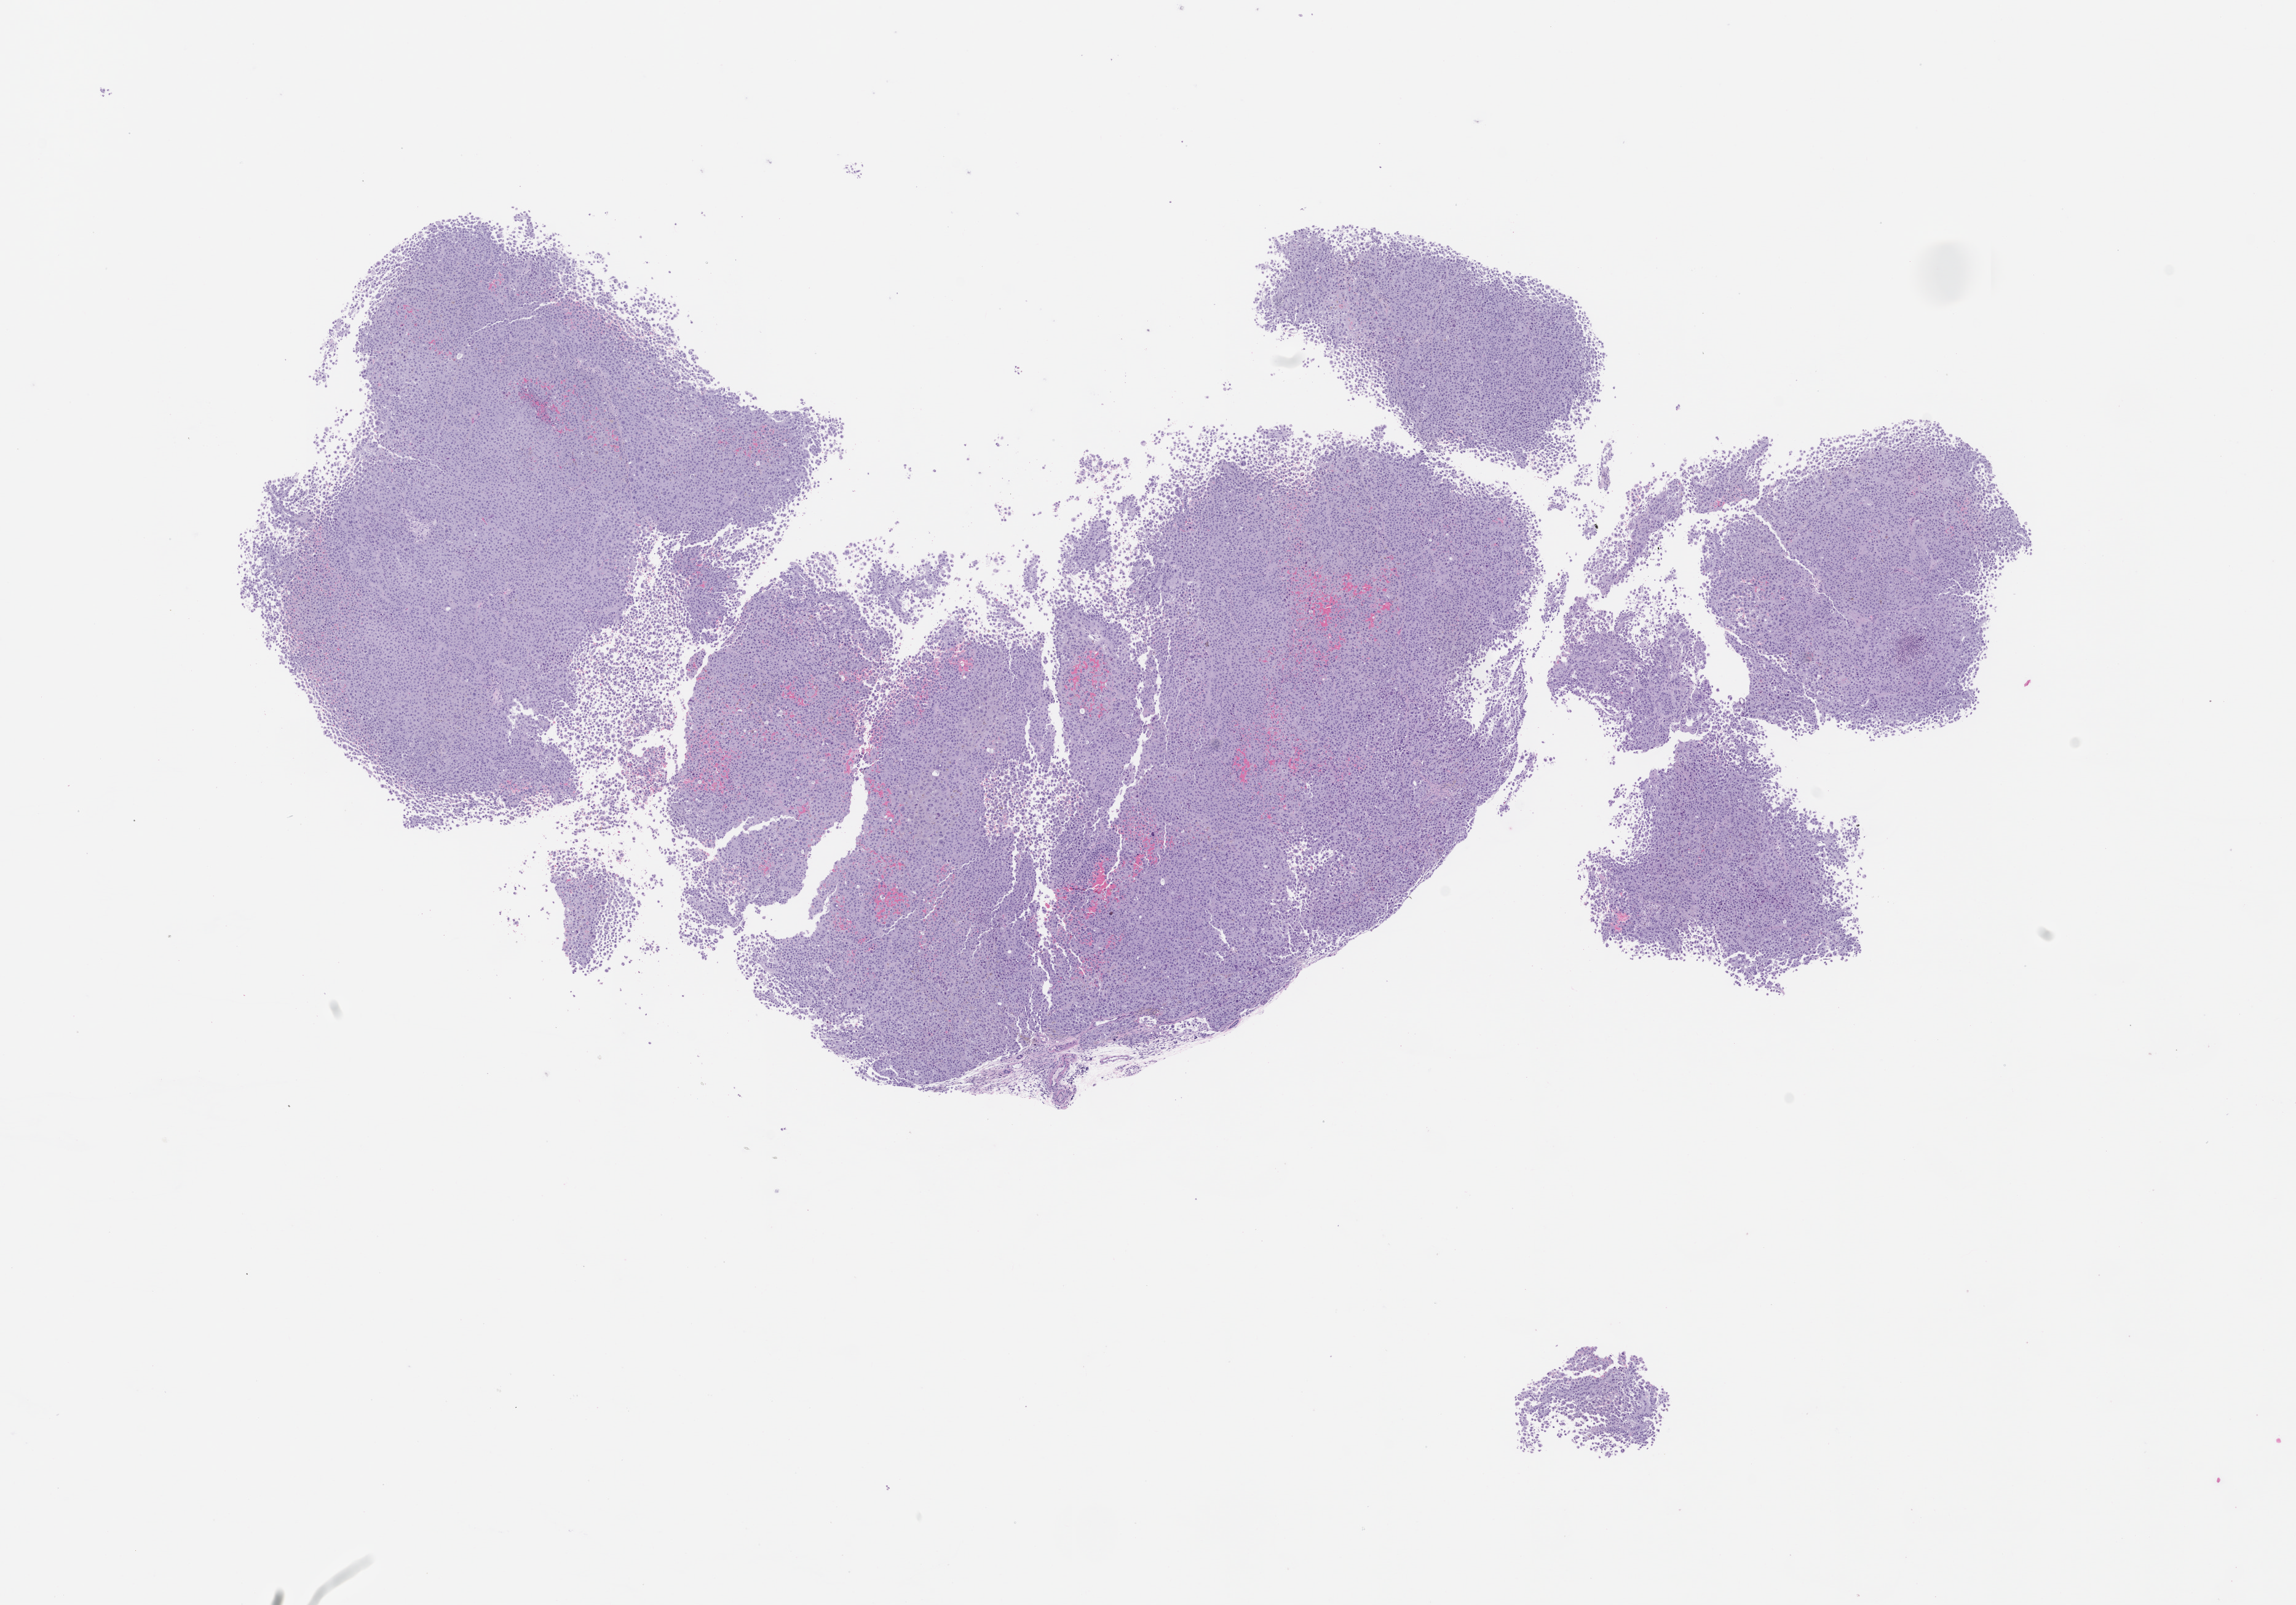
Whole-slide image, H&E: patient-derived xenograft (human tumor grown in a mouse), passage 2, whole scanned area (about 15.0 x 10.5 mm) shown as a low-resolution overview. FFPE section. Originating tumor site category: skin.
Originating patient diagnosis: Melanoma.